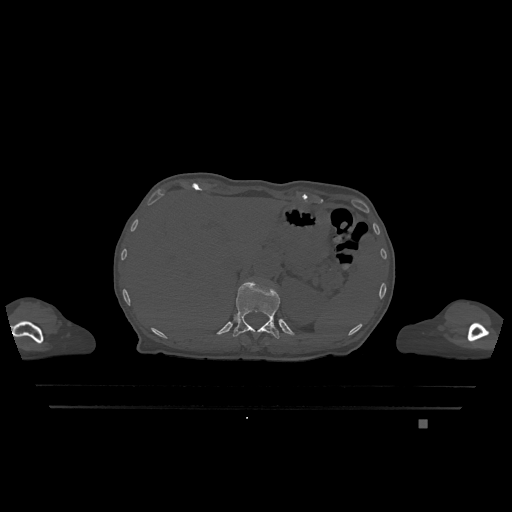
CT including the spine, one axial slice. Slice 533 of 1317 in the series (ordered by position). Bone window (W 1800 / L 400 HU). 0.5 mm slice thickness. 512 × 512 image matrix, field of view 500 × 500 mm. Female patient, age 74 years. Case-level facts recorded for this patient, not image findings: primary cancer: lung; vertebrae with lytic lesions (as recorded): T1, T4, T5, T6, L4, L5.
Structures marked on this image (semi-automatic segmentation, software-assisted and operator-edited):
- T12 vertebra: bounding box <233,281,280,339> (left, top, right, bottom; pixels)